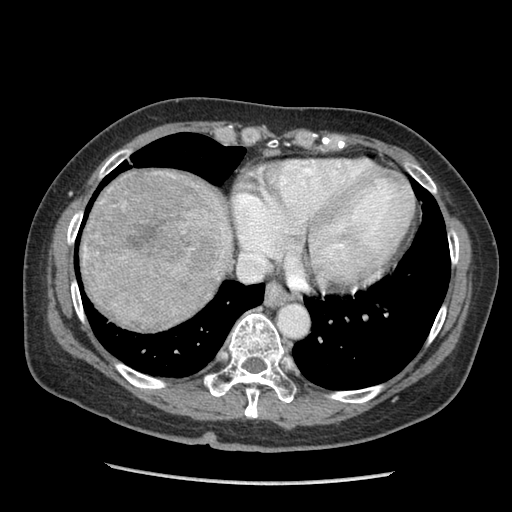
Contrast-enhanced abdominal CT (liver protocol), one axial slice. Reconstruction kernel STANDARD. Soft-tissue window (W 400 / L 40 HU). 2.5 mm slice thickness. 512 × 512 image matrix. From the clinical record (not read from this slice): diagnosis: hepatocellular carcinoma (patient treated with transarterial chemoembolisation; whether this scan precedes or follows treatment is not stated here); TNM stage (as recorded): Stage-I; Child-Pugh class: A; tumour differentiation: moderately differentiated; tumour size: 11.1 cm.
Structures marked on this image (semi-automatically segmented with operator editing):
- liver parenchyma outside the tumour (the mass and vessels are separate outlines, so this box may not span the whole liver): bounding box <80,168,232,326> (left, top, right, bottom; pixels)
- mass: <83,171,234,331>